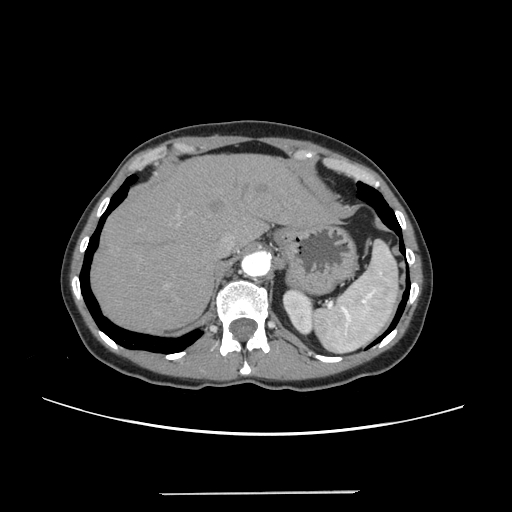
Contrast-enhanced abdominal CT, one axial slice; slice 194 of 240 in the series (ordered by position); 120 kVp; soft-tissue window (W 400 / L 40 HU); 1.25 mm slice thickness; 512 × 512 image matrix, field of view 371 × 371 mm. Female patient, age 60 years. Case-level facts recorded for this patient, not image findings: diagnosis: colorectal cancer liver metastases, imaged before liver resection; multiple liver metastases: no.
Annotated regions visible in this slice (expert manual segmentation):
- hepatic veins: bounding box (x1, y1, x2, y2) in pixels: (221, 235, 234, 252)
- liver: (92, 156, 328, 332)
- planned liver remnant (the part of the liver to remain after resection): (92, 156, 329, 332)
- portal vein (with intrahepatic branches): (164, 285, 170, 287)